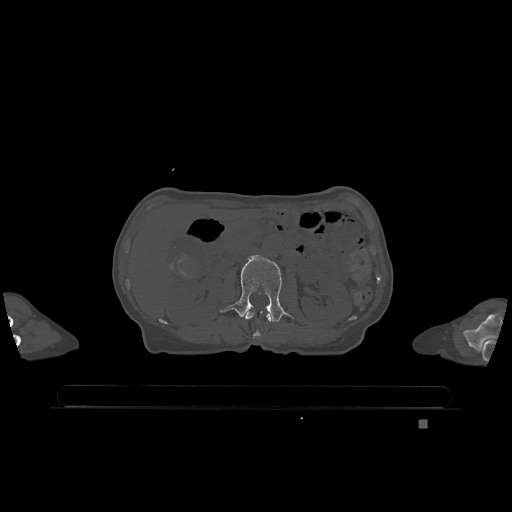
CT including the spine, one axial slice. Bone window (W 1800 / L 400 HU). 0.5 mm slice thickness. 512 × 512 image matrix, field of view 500 × 500 mm. Female patient, age 74 years. From the clinical record (not read from this slice): primary cancer: lung; vertebrae with lytic lesions (as recorded): T1, T4, T5, T6, L4, L5.
Outlined on this slice (semi-automatically segmented with operator editing):
- L1 vertebra: bounding box <243,311,272,338> (left, top, right, bottom; pixels)
- L2 vertebra: <219,255,292,322>